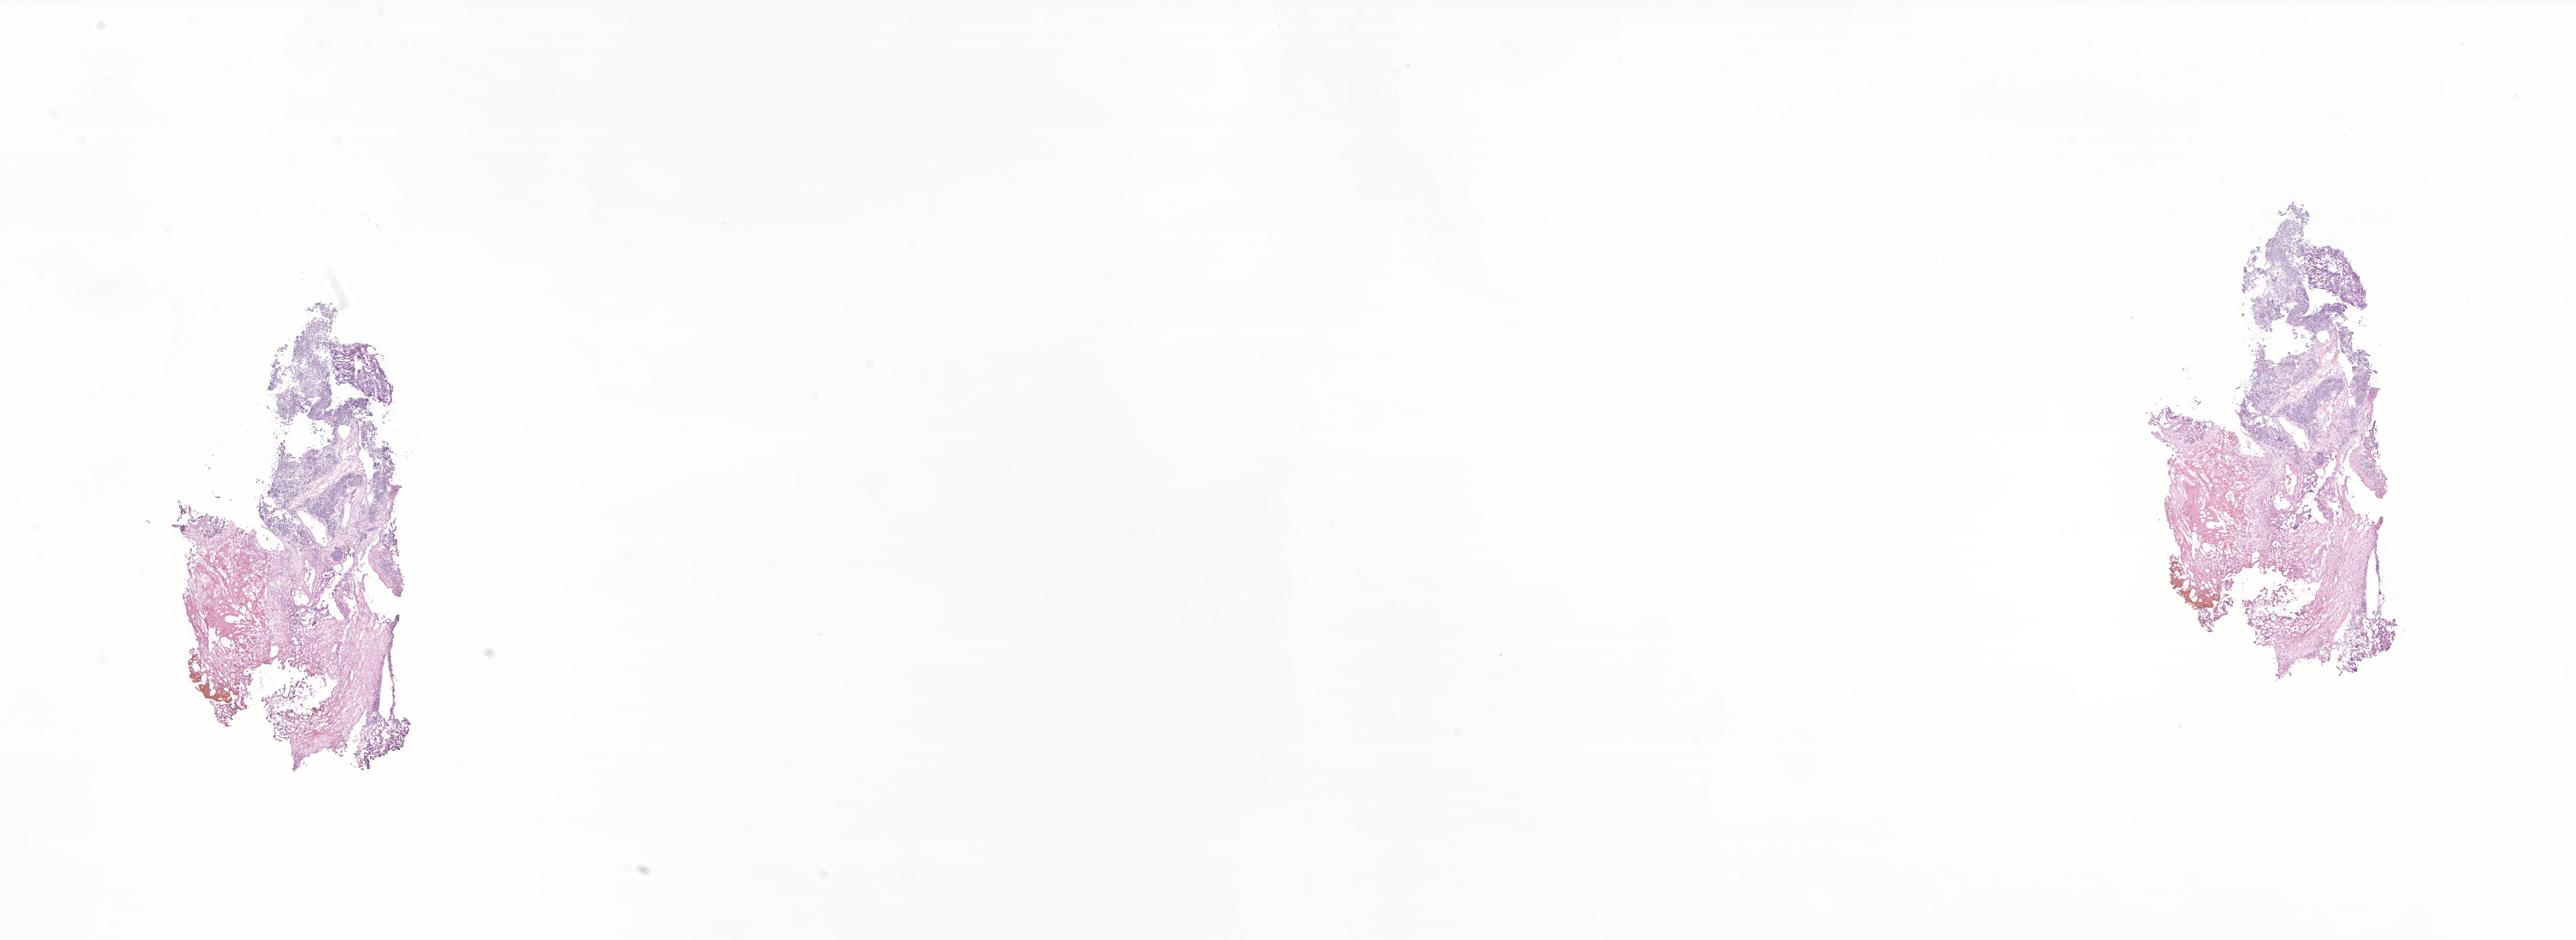
Whole-slide image, H&E stain of tumor tissue from the abdomen — a low-resolution overview of the entire scanned area, about 26.8 x 9.8 mm. Frozen section. Patient: female, age 81 months (6 years 9 months).
- recorded diagnosis: Neuroblastoma, NOS